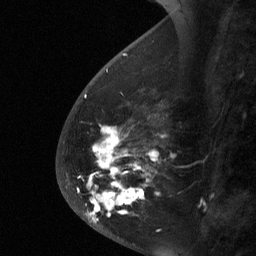
Breast MRI (dynamic contrast-enhanced), one sagittal slice; position 22 of 64 along the scan axis; dynamic contrast-enhanced study with each time point stored as its own series, time point 2 of 3 at this slice position (early post-contrast, ordered by acquisition time); 1.5 T; TE 4.8 ms, TR 27 ms; 2 mm slice thickness; 256 × 256 image matrix, field of view 180 × 180 mm. Female patient, age 56 years. Case-level facts recorded for this patient, not image findings: setting: breast cancer imaged before/during neoadjuvant chemotherapy; receptor status: HER2-positive.
Structures marked on this image (semi-automatic segmentation, software-assisted and operator-edited):
- analysis volume of interest (the breast-tissue region the enhancement analysis was run in; not a lesion): bounding box <59,104,169,229> (left, top, right, bottom; pixels)
- tumour enhancement mask (voxels above the 90 % enhancement threshold inside the analysis volume of interest): <86,128,156,223>